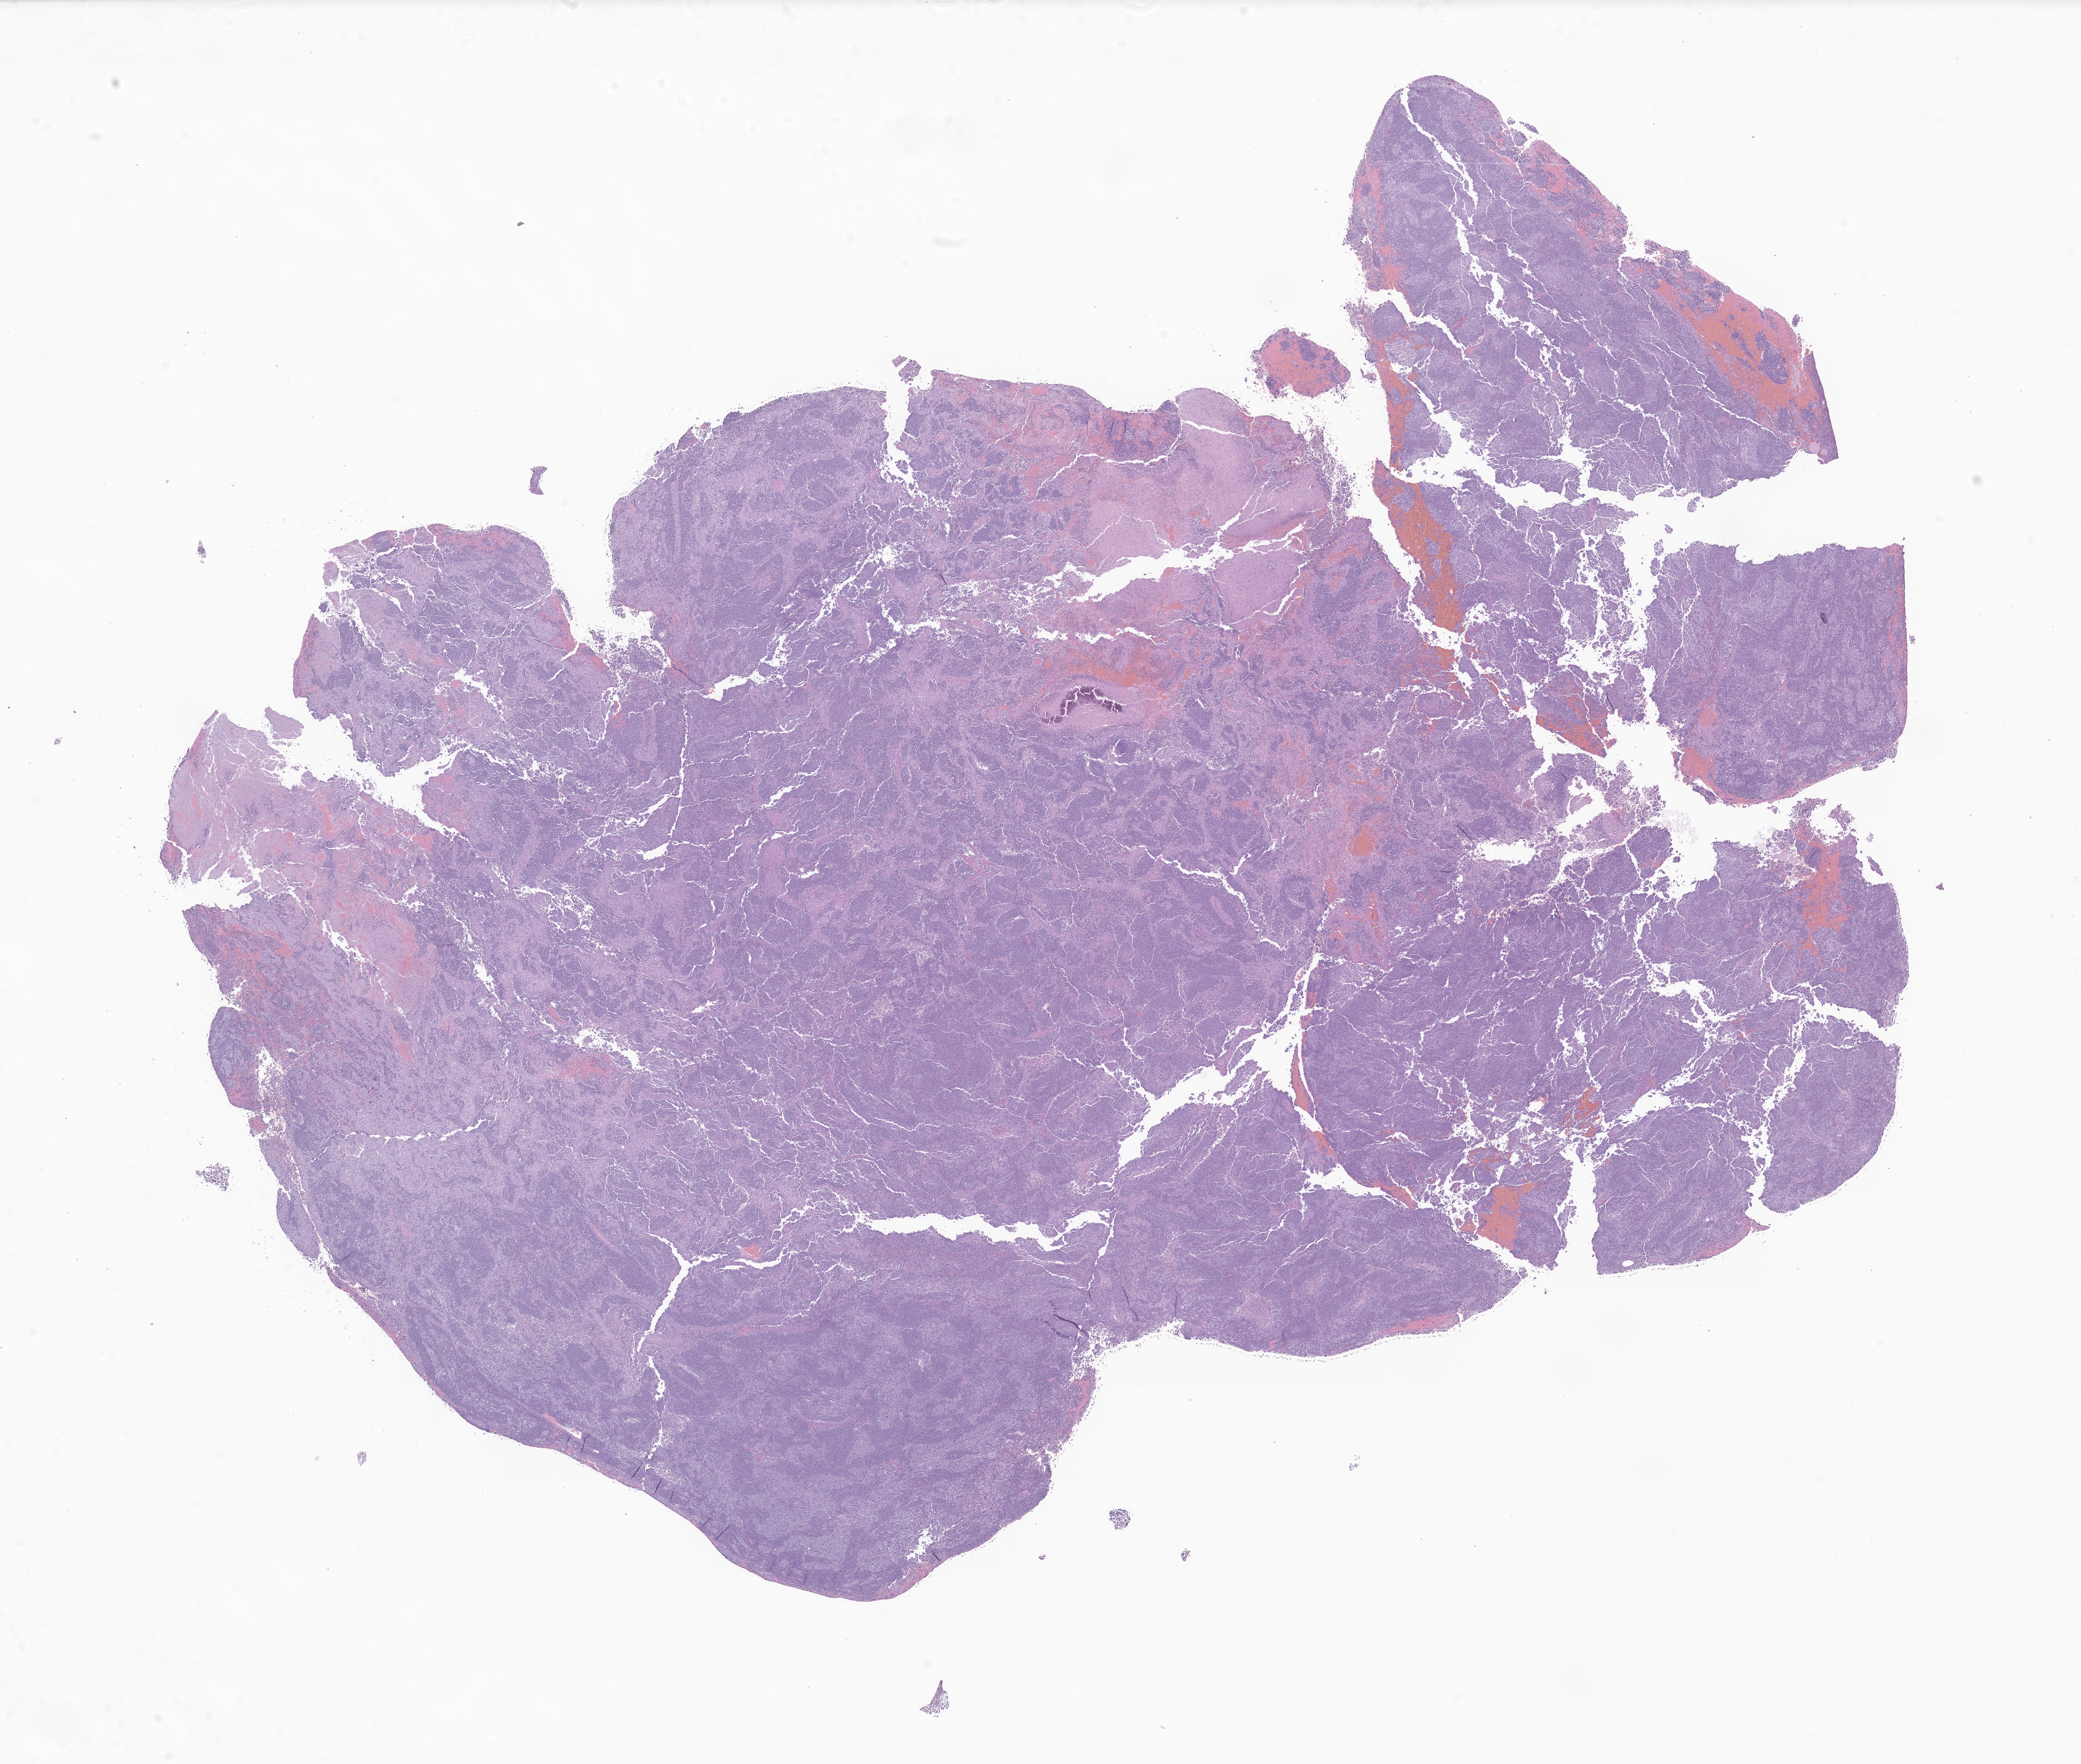
Digitized H&E-stained section of tumor tissue from the brain — shown as a low-resolution overview of the whole scanned area (about 23.5 x 20.0 mm), formalin-fixed, paraffin-embedded (FFPE) tissue. Patient female; age 53 months (4 years 5 months).
Diagnosis (ICD-O-3 morphology term): Neoplasm, uncertain whether benign or malignant.